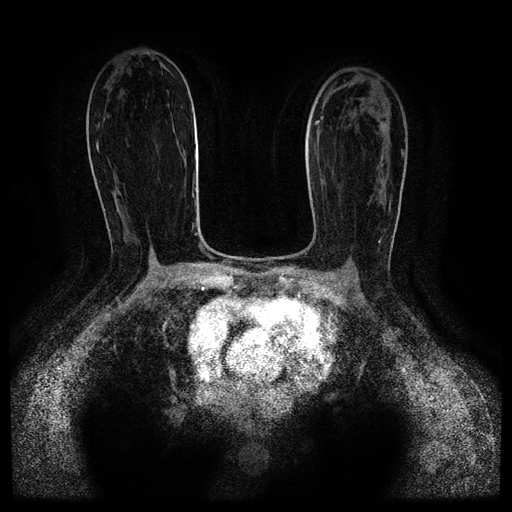
Breast MRI (dynamic contrast-enhanced, multi-phase), one axial slice. Position 58 of 116 along the scan axis. Dynamic contrast-enhanced series, time point 2 of 5 at this slice position (early post-contrast). 1.5 T. TE 2.6 ms, TR 5.3 ms. 2 mm slice thickness. 512 × 512 image matrix. Female patient, age 52 years.
Outlined on this slice (semi-automatically segmented with operator editing):
- breast lesion (labelled 'tumour' in the annotation; benign lesions carry a separate 'benign' label): bounding box <380,123,388,132> (left, top, right, bottom; pixels)